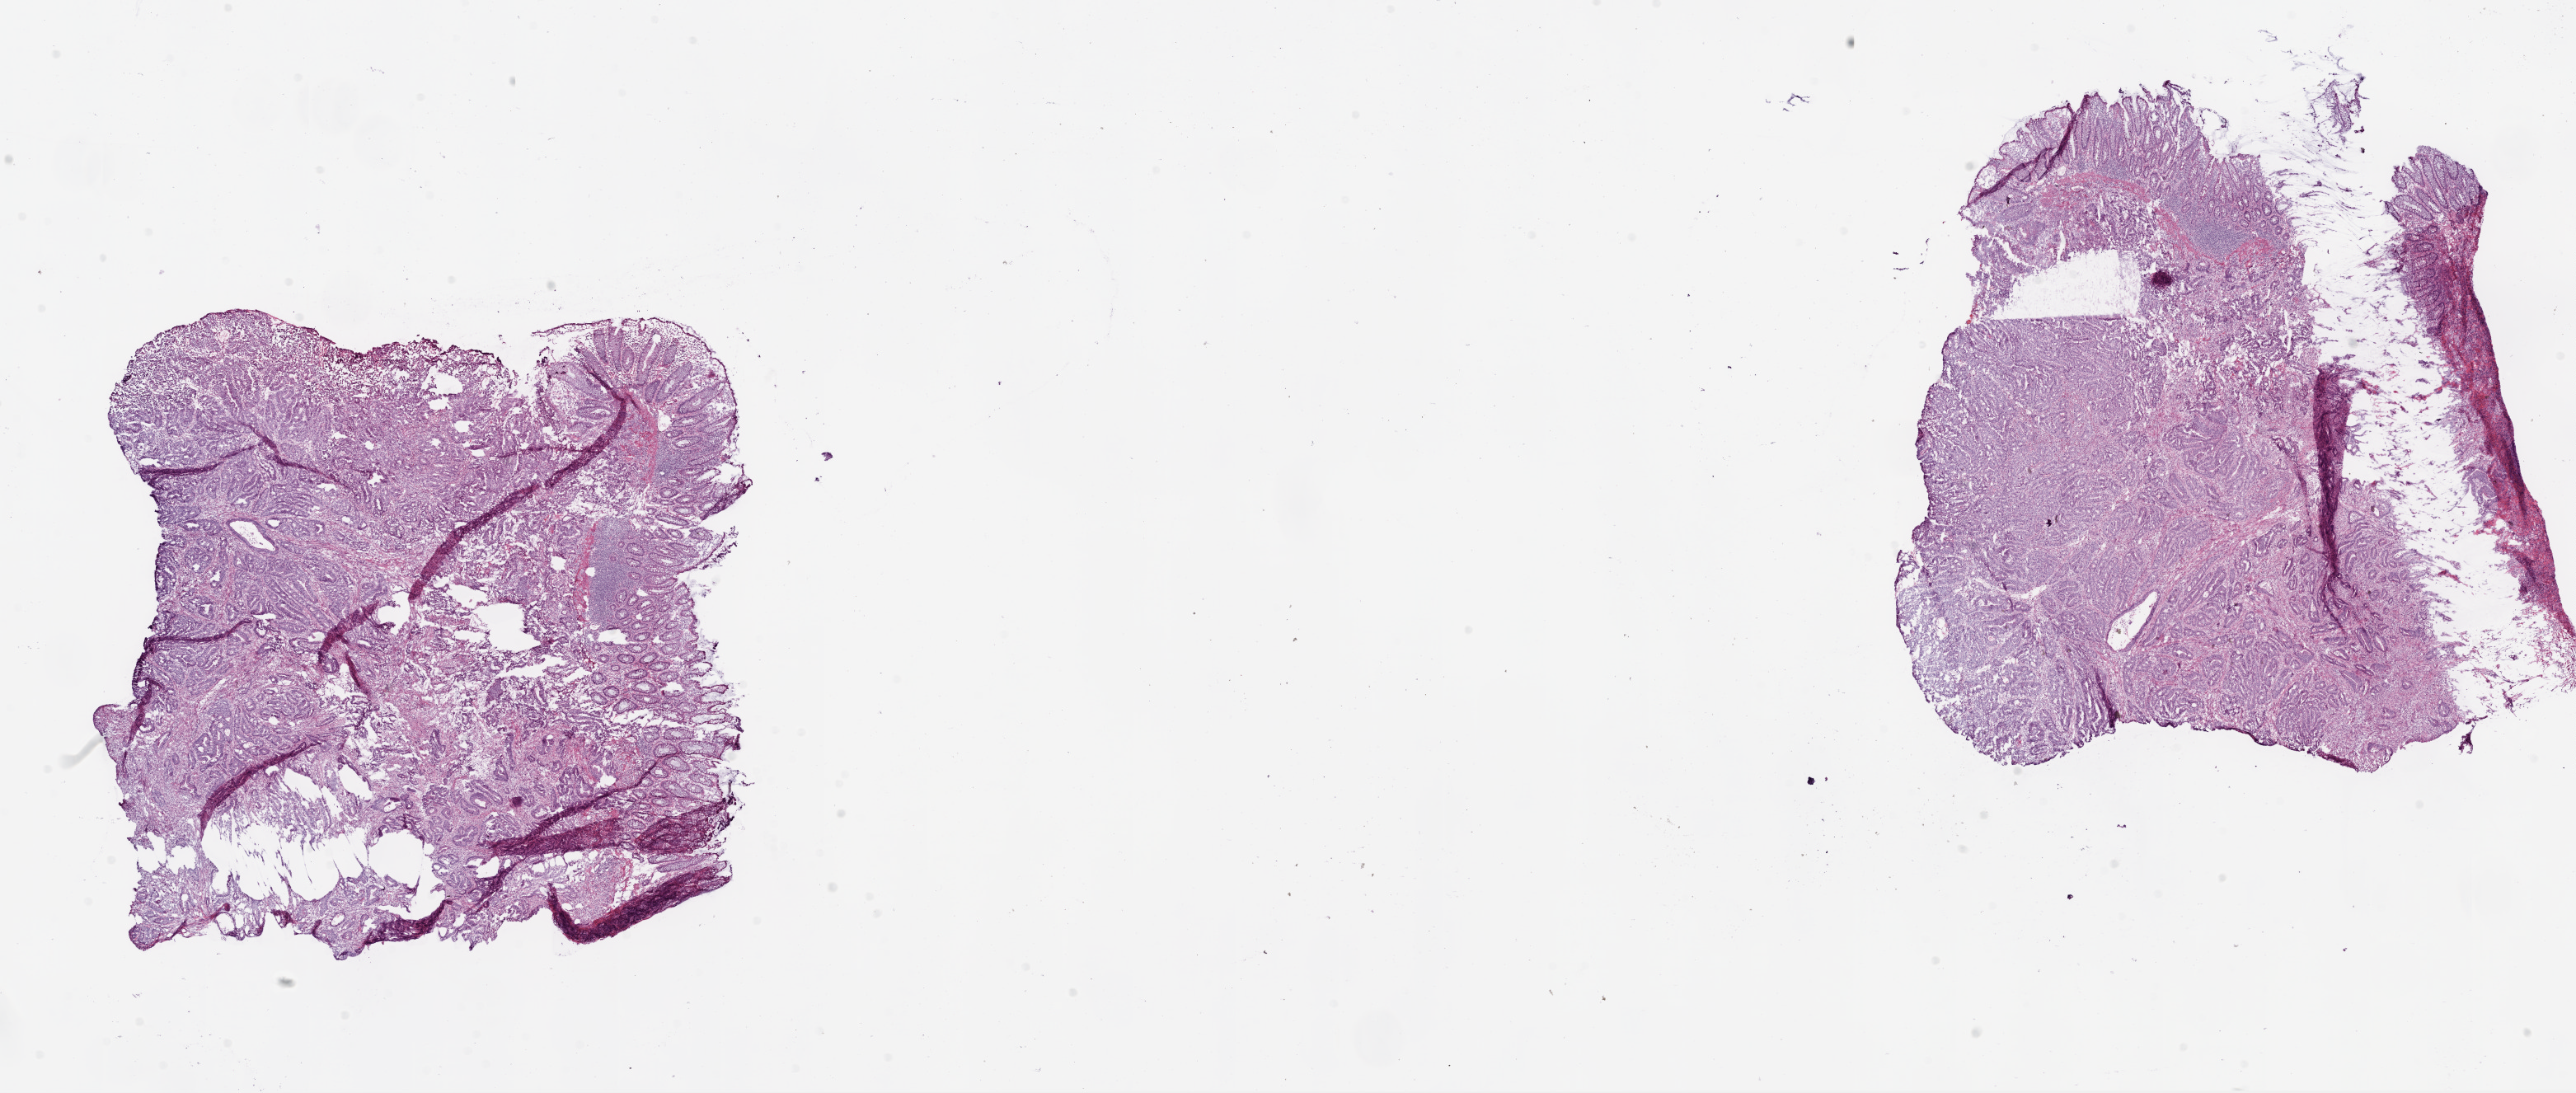
H&E whole-slide image — shown as a low-resolution overview of the whole scanned area (about 25.1 x 10.6 mm), frozen section, sample: primary tumour, rectum. Male patient; age at initial diagnosis 64 years. Pathologist review of this section (percent, as recorded): tumour cells 70%, tumour nuclei 75%, normal cells 15%, stromal cells 10%, necrosis 5%.
* lymph nodes positive (case pathology): 0 of 15 examined
* histologic diagnosis: Adenocarcinoma, NOS
* AJCC pathologic stage: I (6th edition)